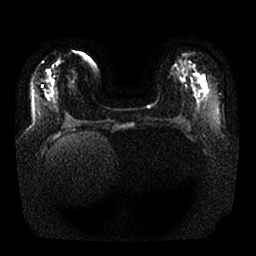
Breast MRI, one axial slice. Position 10 of 25 along the scan axis. Diffusion-weighted series; image 2 of 4 stored at this slice position (different b-values; order by instance number). 1.5 T. 4 mm slice thickness. 256 × 256 image matrix, field of view 350 × 350 mm. Female patient.
Outlined on this slice (manually delineated by an expert):
- tumour on diffusion-weighted imaging: bounding box [x1, y1, x2, y2] px = [199, 81, 206, 88]